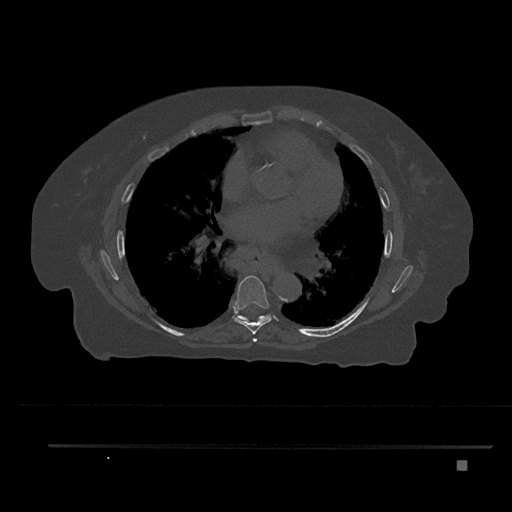
CT including the spine, one axial slice; slice 477 of 797 in the series (ordered by position); 120 kVp; bone window (W 1800 / L 400 HU); 0.5 mm slice thickness; 512 × 512 image matrix, field of view 437 × 437 mm. Female patient, age 76 years. From the clinical record (not read from this slice): primary cancer: lung; vertebrae with lytic lesions (as recorded): T11, L3.
Outlined on this slice (semi-automatically segmented with operator editing):
- T6 vertebra: bounding box [x1, y1, x2, y2] px = [253, 338, 257, 342]
- T7 vertebra: [233, 275, 272, 335]
- T8 vertebra: [235, 313, 270, 321]